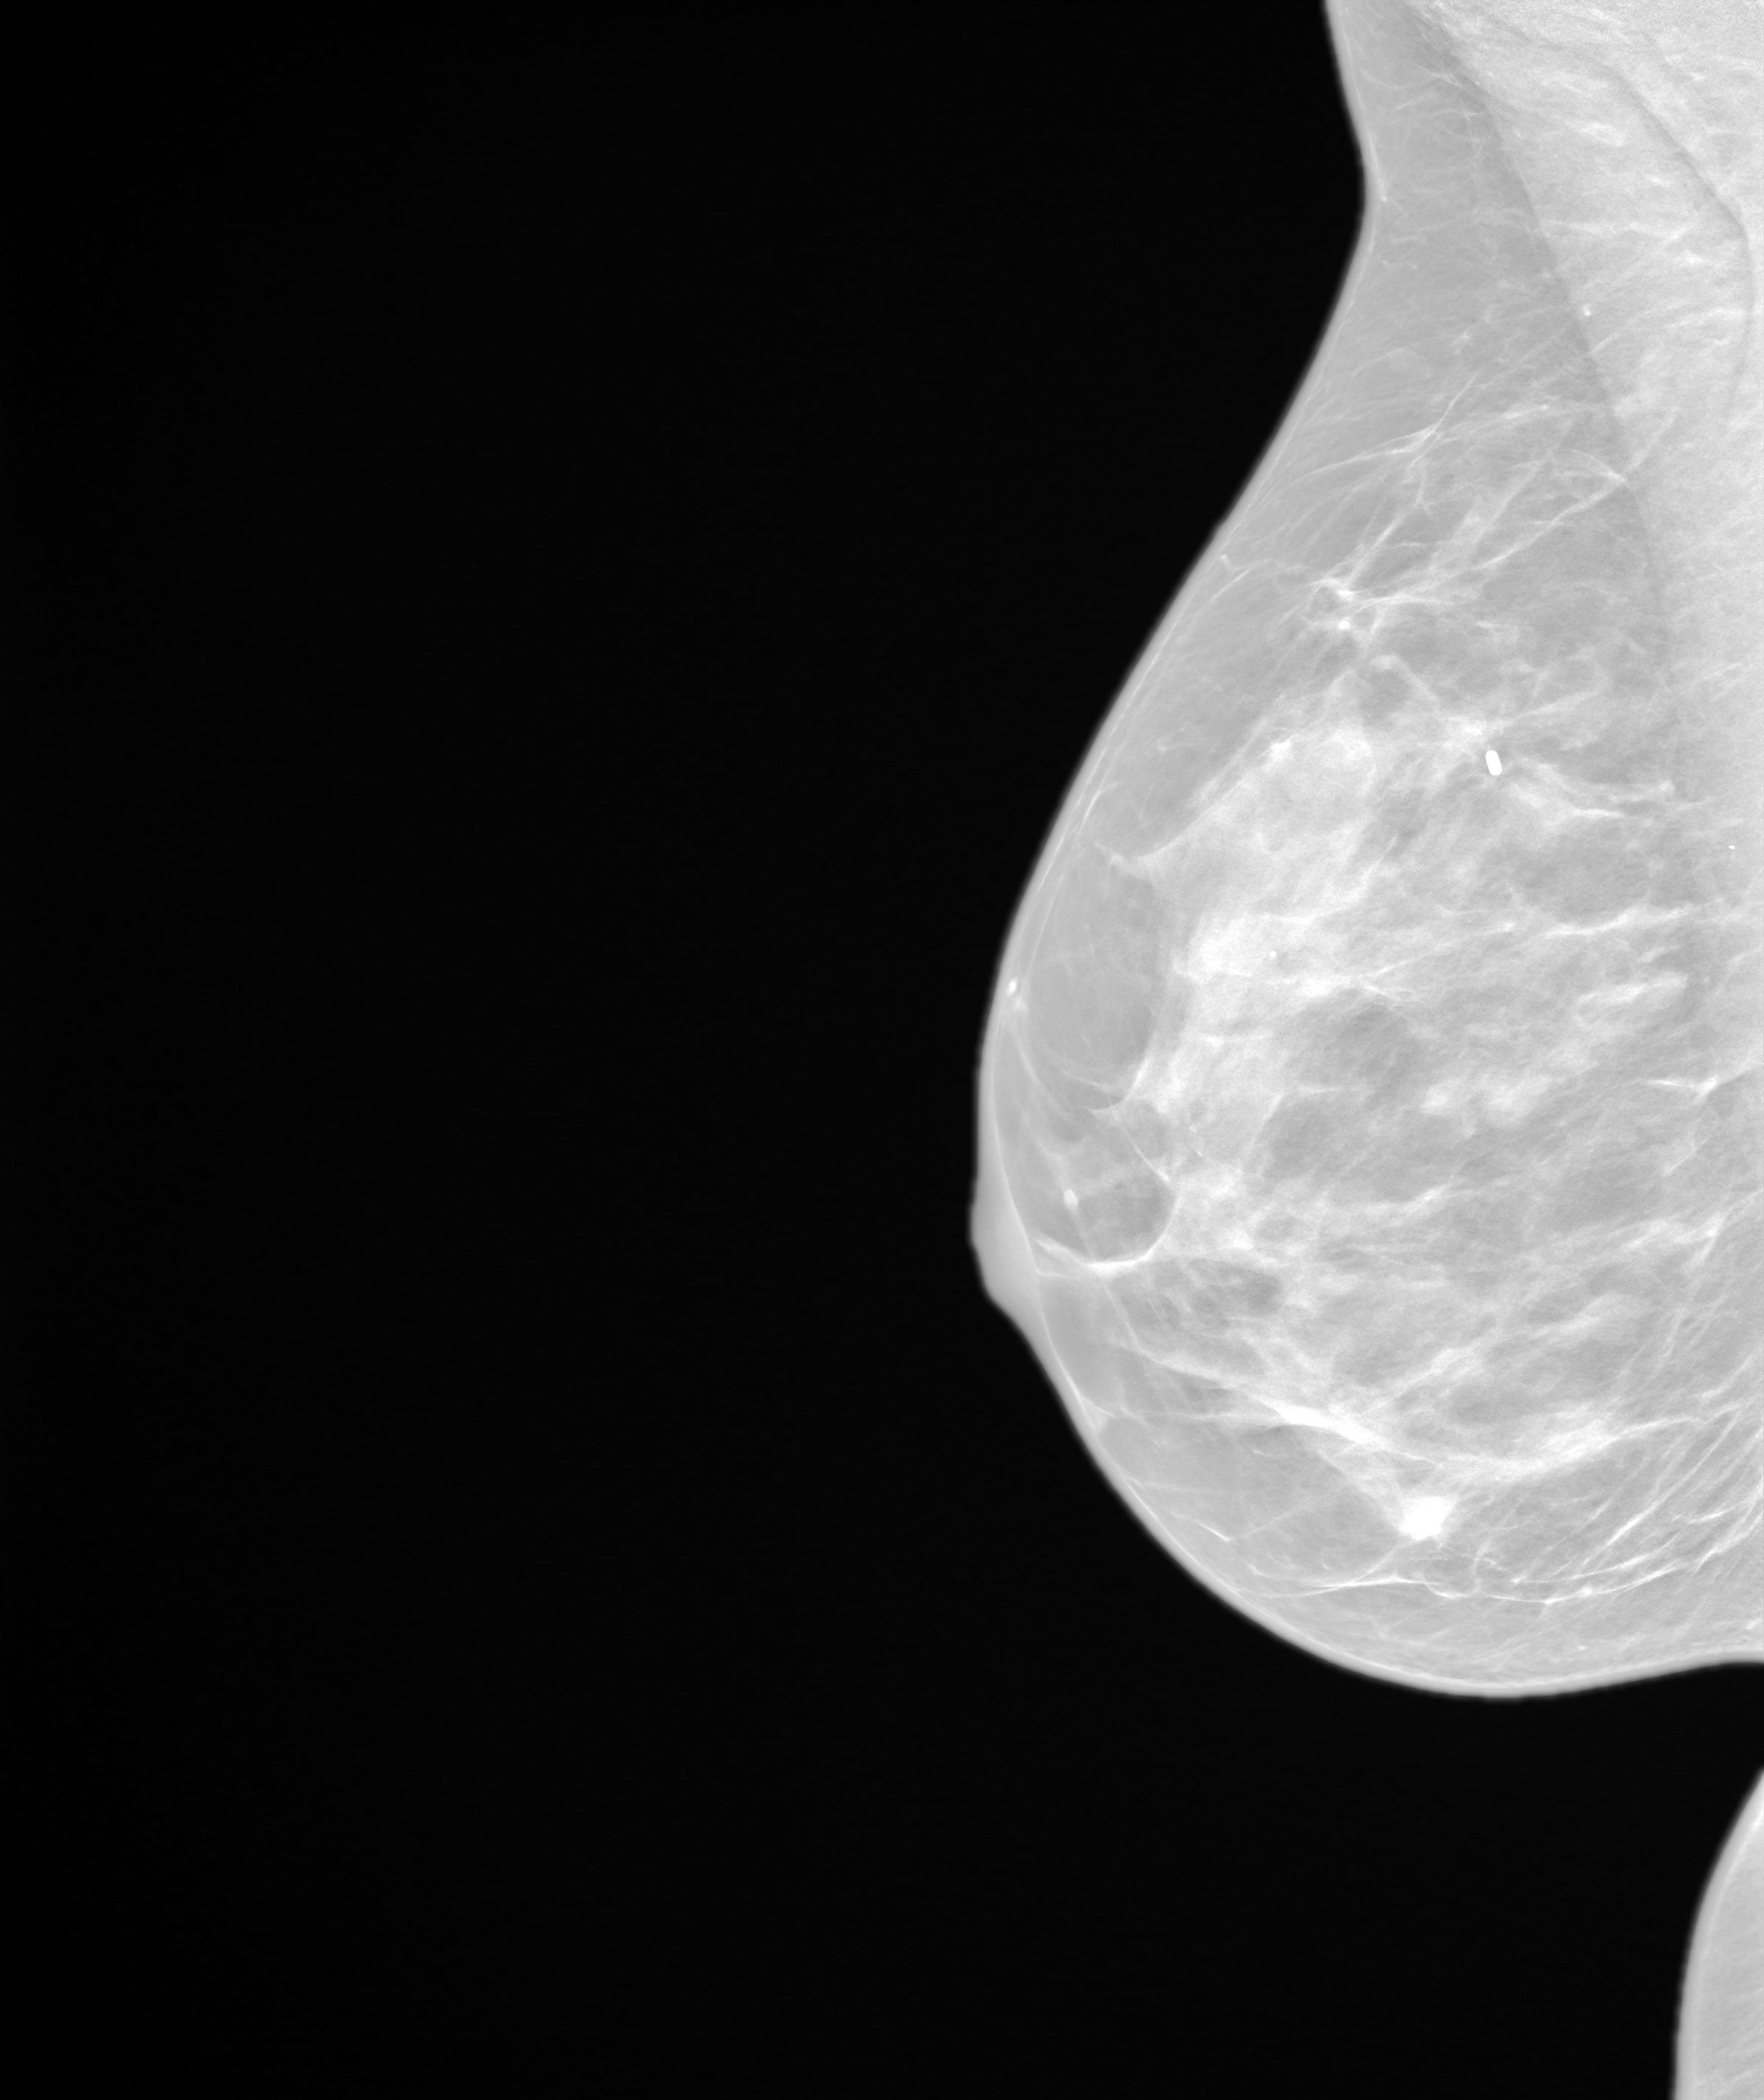
Screening examination, system: SenoIris_1SP2(440). Female patient, age 52 years.
Image type: synthesized 2-D view from tomosynthesis. Breast: right. Projection: mediolateral oblique (MLO) view.